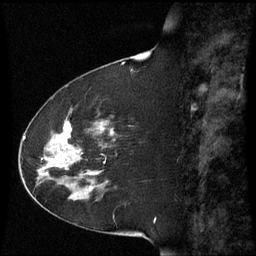
Breast MRI (dynamic contrast-enhanced), one sagittal slice. Slice 21 of 60 in the series (ordered by position). Dynamic contrast-enhanced series, image 2 of 3 at this slice position (ordered by acquisition). 1.5 T. TE 4.2 ms, TR 8.9 ms. 2.3 mm slice thickness. 256 × 256 image matrix, field of view 210 × 210 mm. Female patient, age 51 years. From the clinical record (not read from this slice): setting: breast cancer imaged before/during neoadjuvant chemotherapy; receptor status: HR-positive, HER2-negative.
Annotated regions visible in this slice (semi-automatic segmentation, software-assisted and operator-edited):
- analysis volume of interest (the breast-tissue region the enhancement analysis was run in; not a lesion): box from (x=50, y=120) to (x=116, y=187) px
- tumour enhancement mask (voxels above the 70 % enhancement threshold inside the analysis volume of interest): (x=53, y=123)–(x=114, y=162)